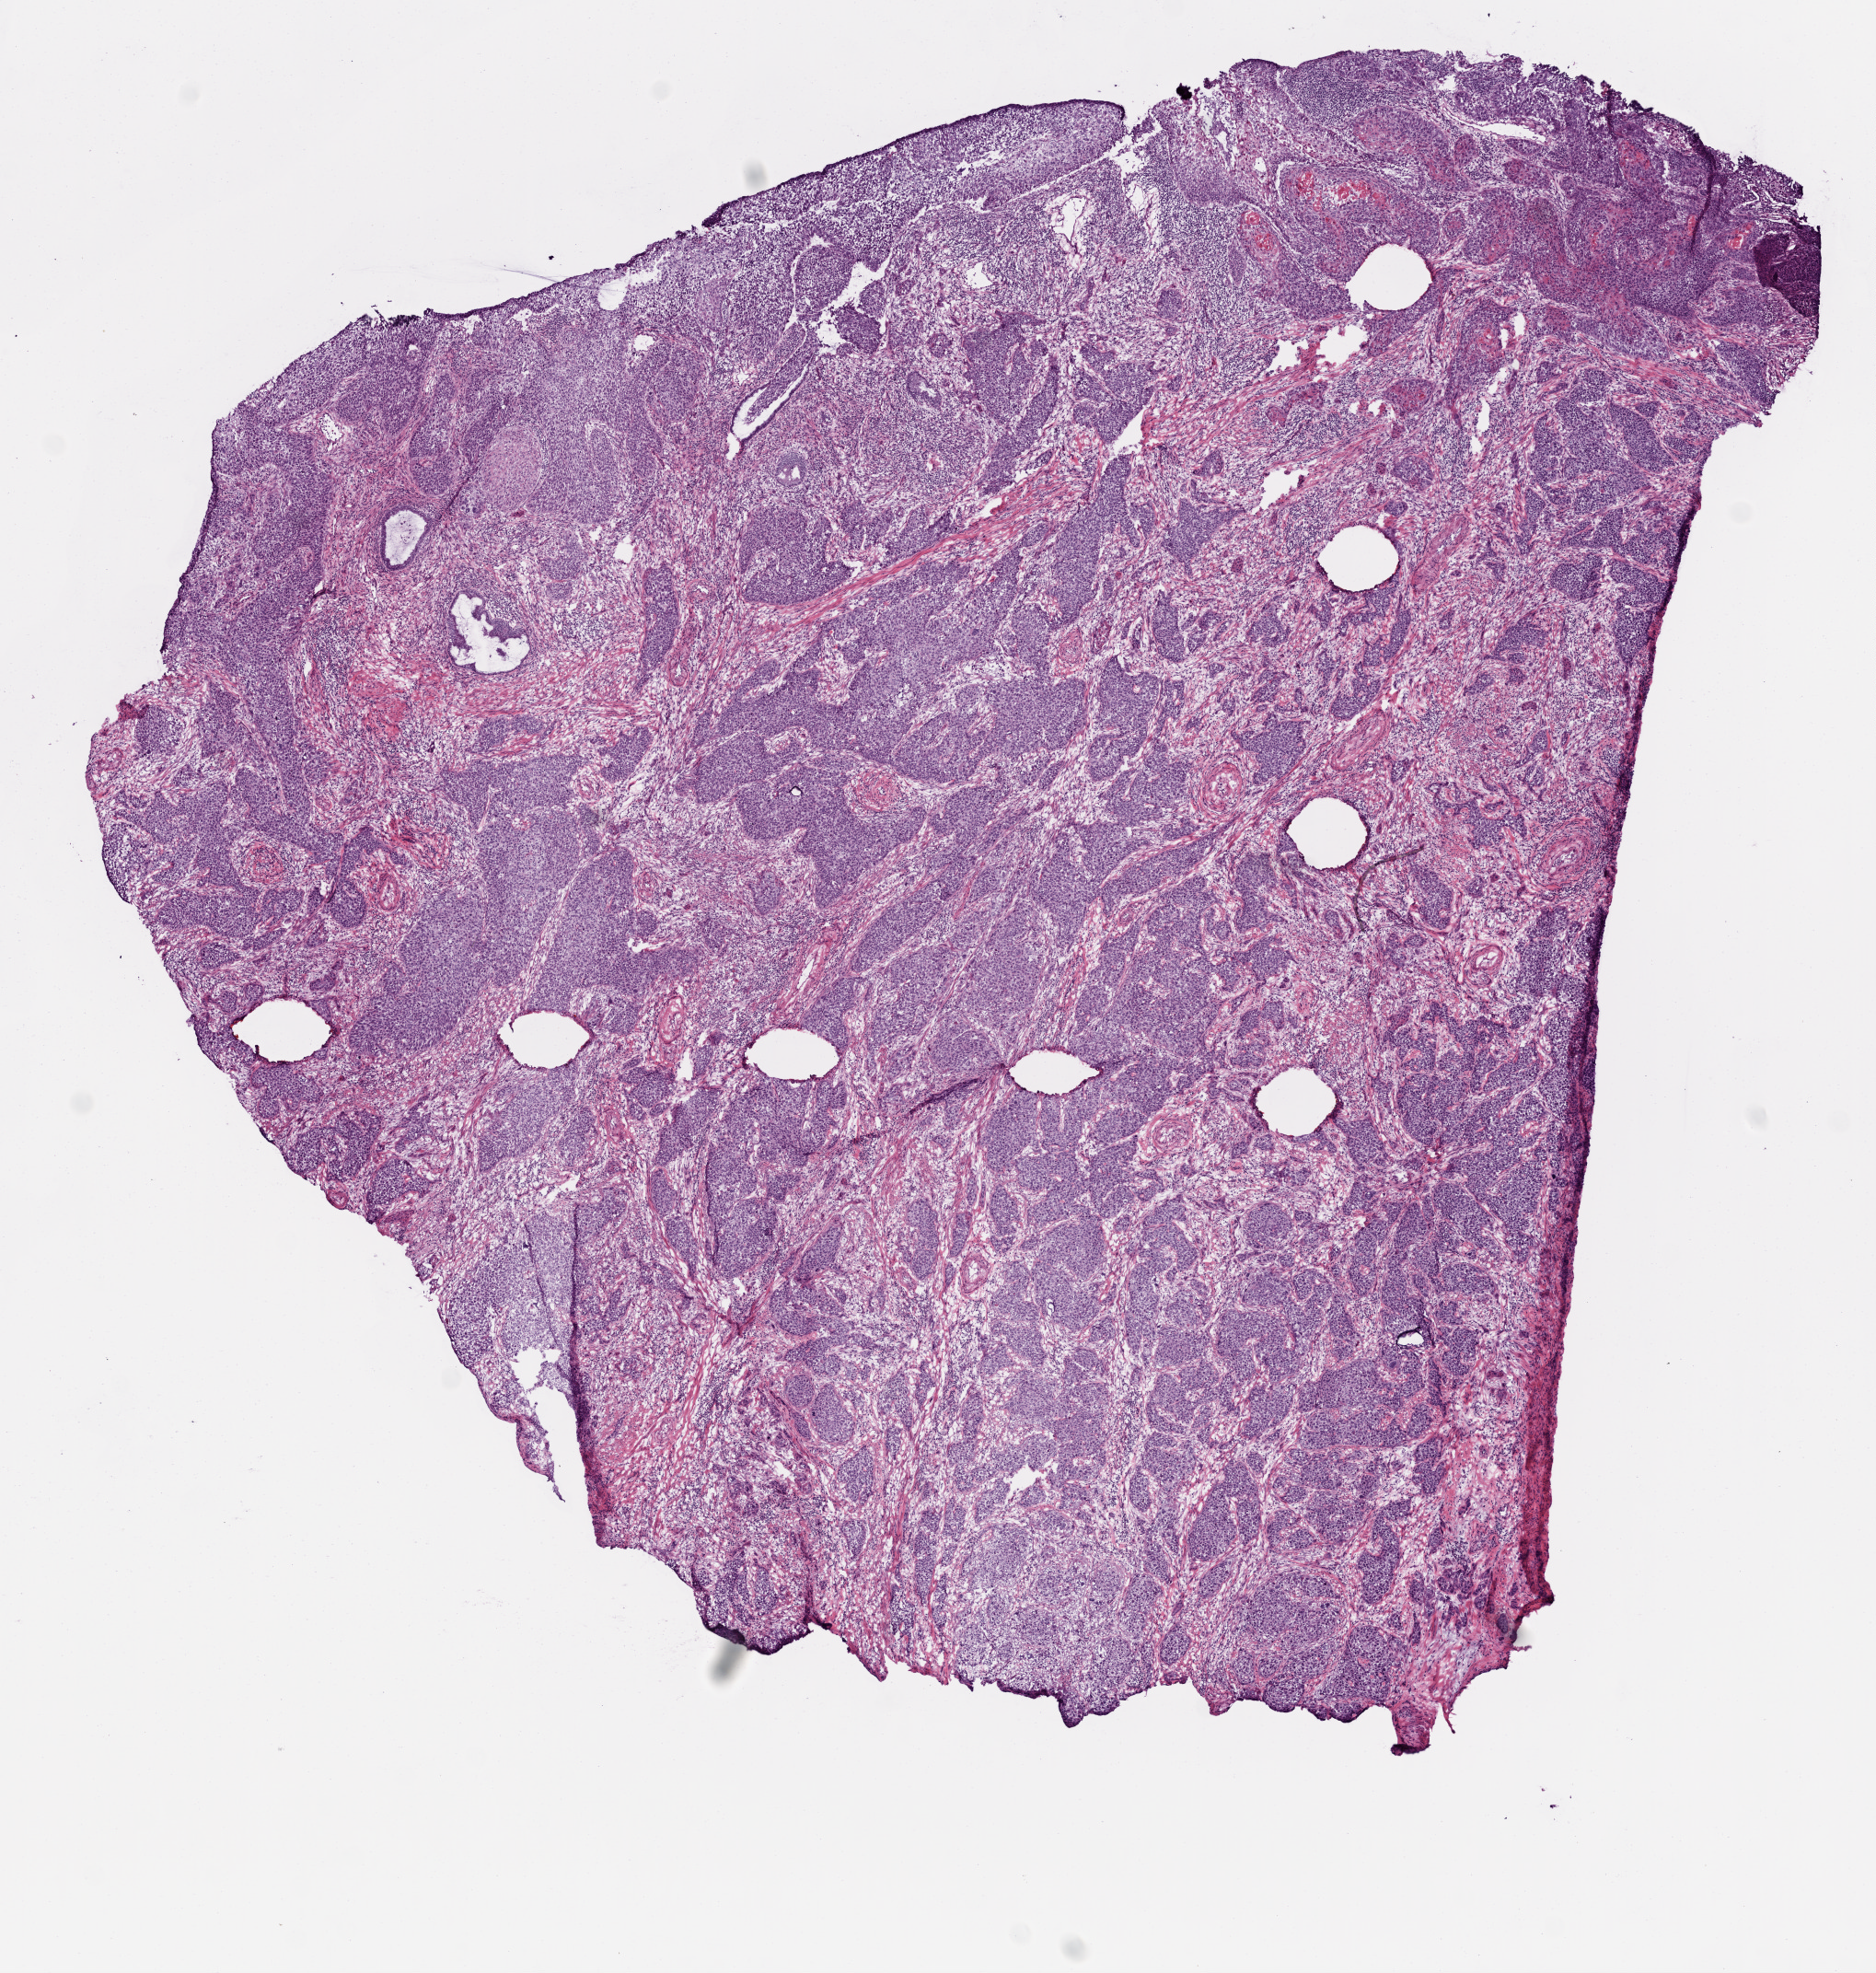
H&E-stained whole-slide image, shown as a low-resolution overview of the whole scanned area (about 8.2 x 8.6 mm); frozen section; sample: primary tumour, cervix. Female, age 45 years at initial diagnosis. Histologic grade: G2 (moderately differentiated). Slide review estimates, as recorded: tumour cells 90%, tumour nuclei 80%, normal cells 0%, stromal cells 5%, necrosis 5%. Infiltration values recorded for this section: lymphocyte infiltration 0%, monocyte infiltration 0%, neutrophil infiltration 0%.
* histologic diagnosis: Squamous cell carcinoma, keratinizing, NOS (cervix uteri)
* FIGO stage: IB1